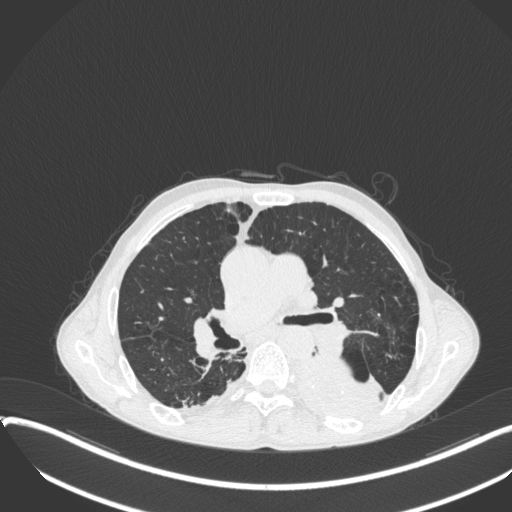
Chest CT, one axial slice; slice 221 of 400 in the series (ordered by position); lung window (W 1500 / L -600 HU); 512 × 512 image matrix. Male patient, age 57 years. From the clinical record (not read from this slice): clinical TNM (as recorded): T4 N0 M0.
Annotated regions visible in this slice (bounding box drawn by a radiologist):
- lung tumour (recorded histology: squamous cell carcinoma): box from (x=290, y=353) to (x=383, y=421) px